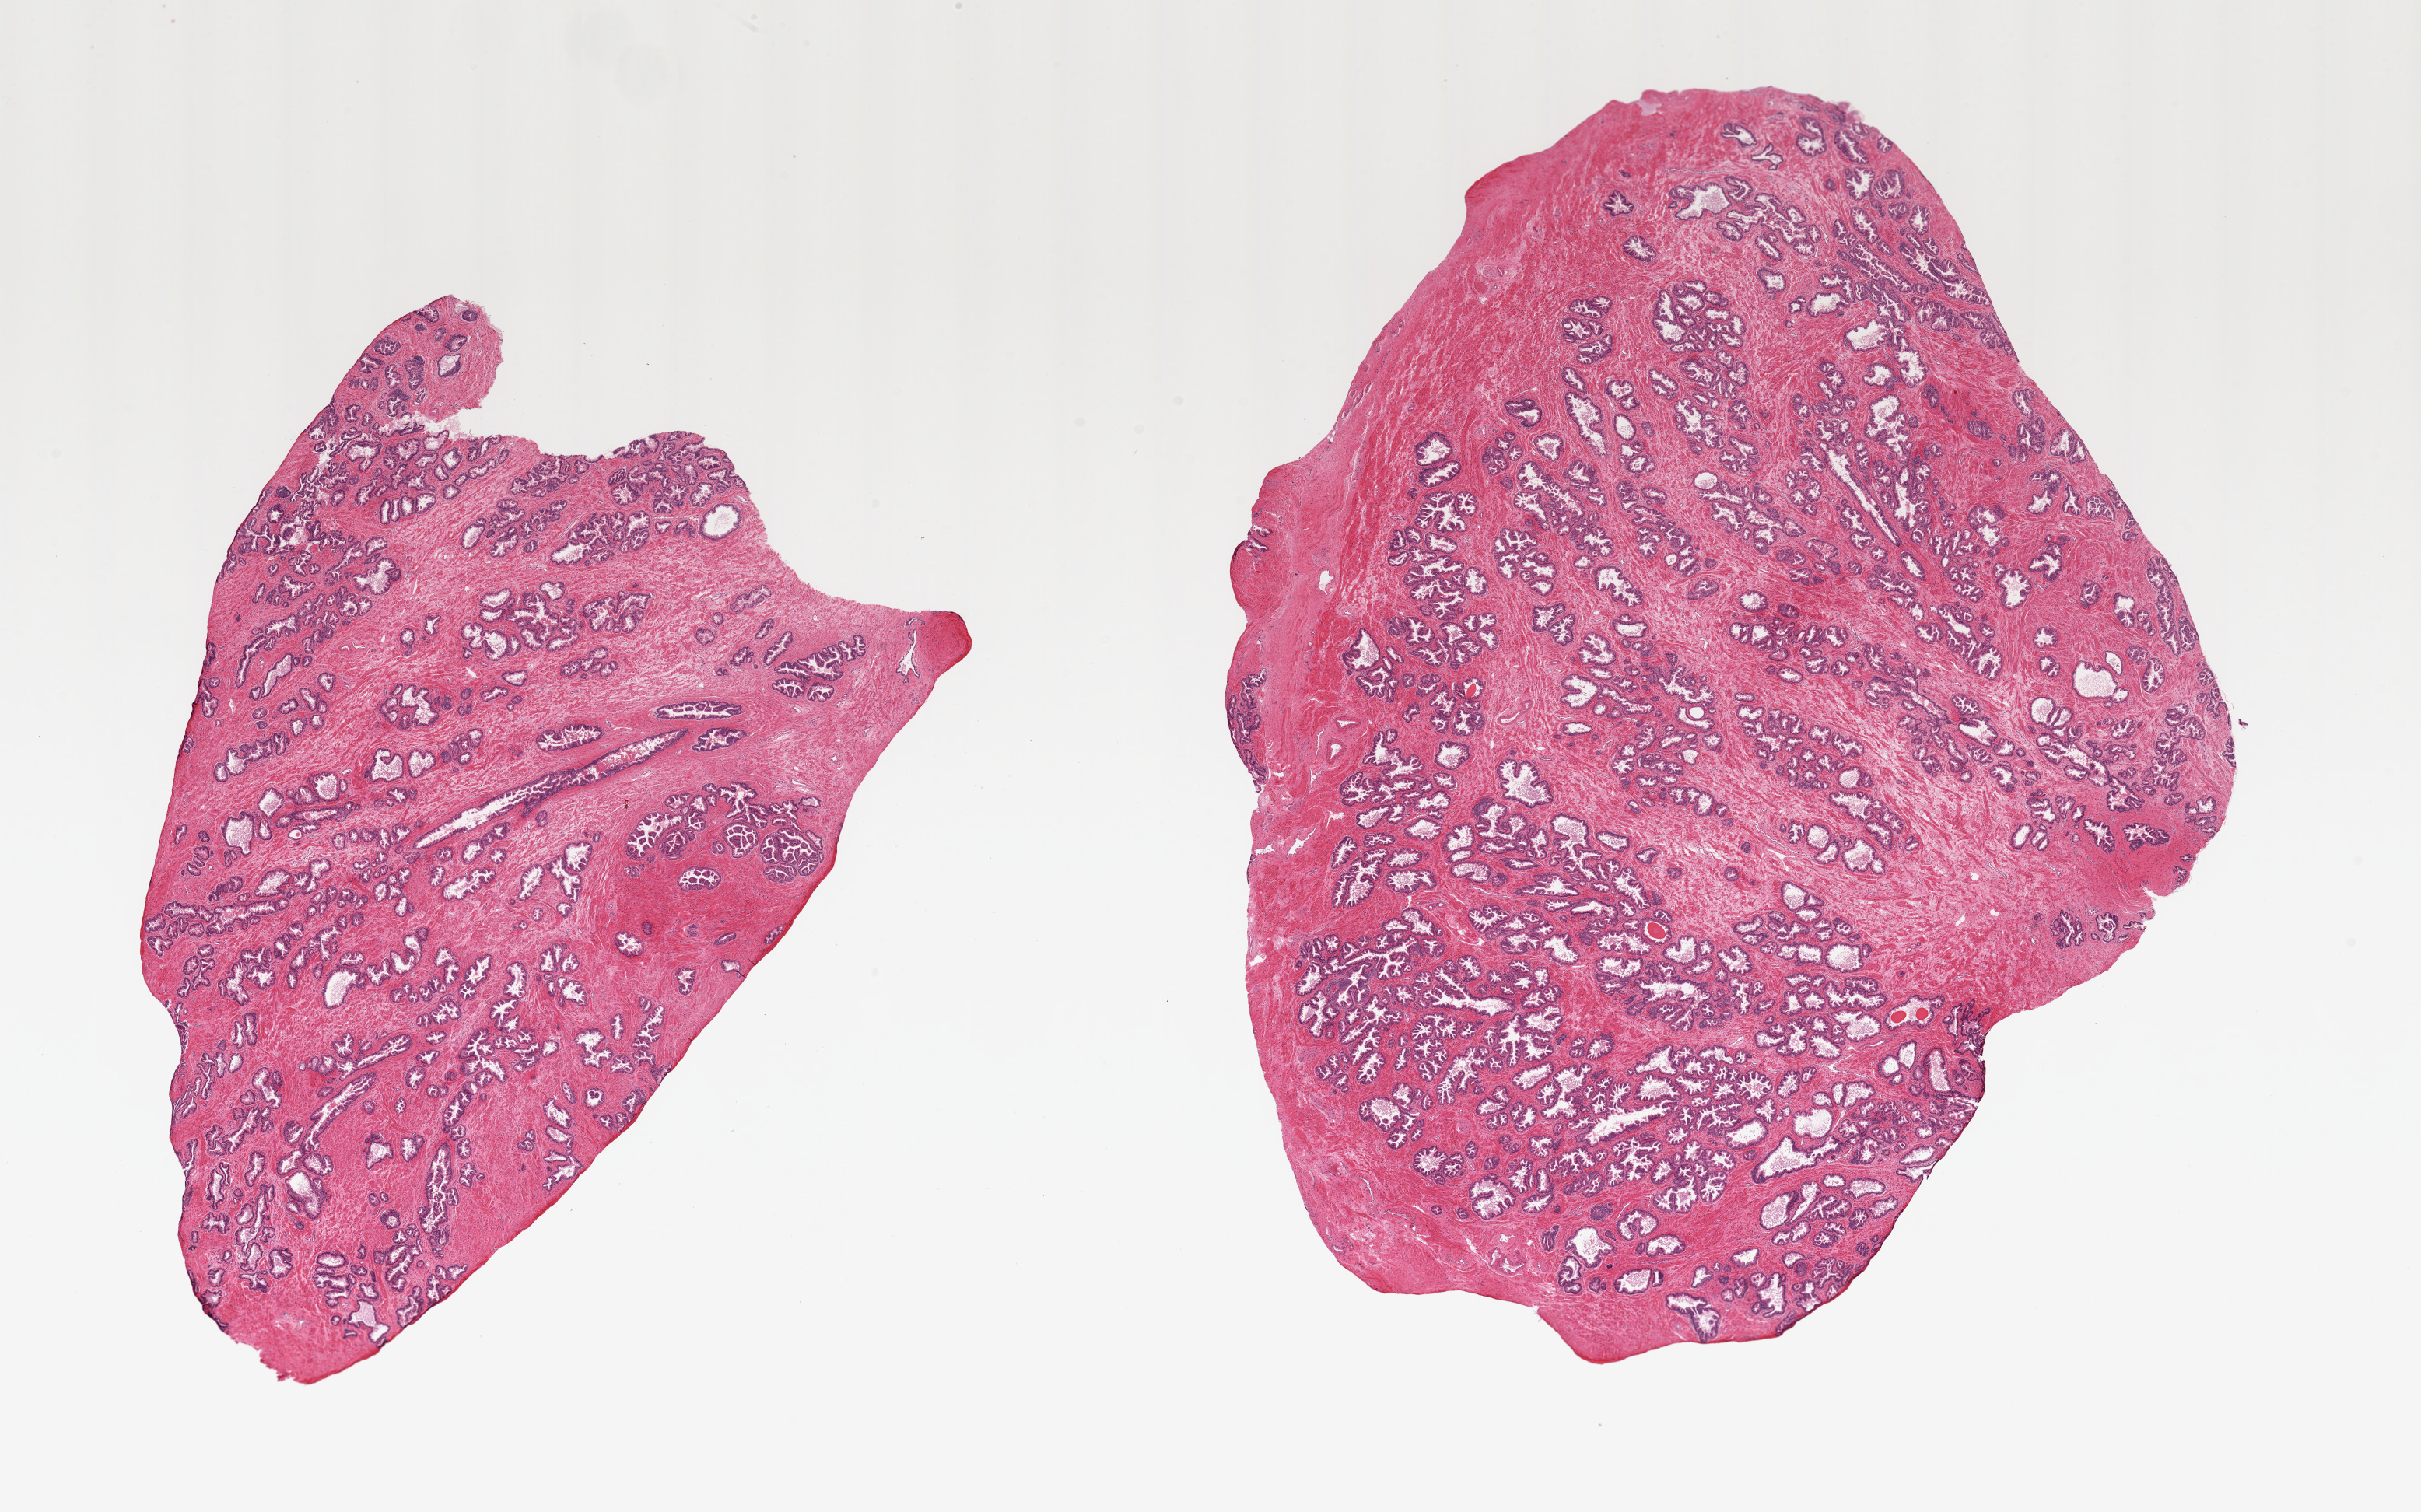
Whole-slide image, hematoxylin and eosin (H&E) stain, brightfield, whole scanned area (about 24.6 x 15.4 mm, acquisition: 20x scan) shown as a low-resolution overview, PAXgene-fixed, paraffin-embedded tissue, section of prostate (target tissue), tissue donor sample. Male donor.
Reviewer comment on this tissue sample: 2 pieces; excellent specimen, well preserved.